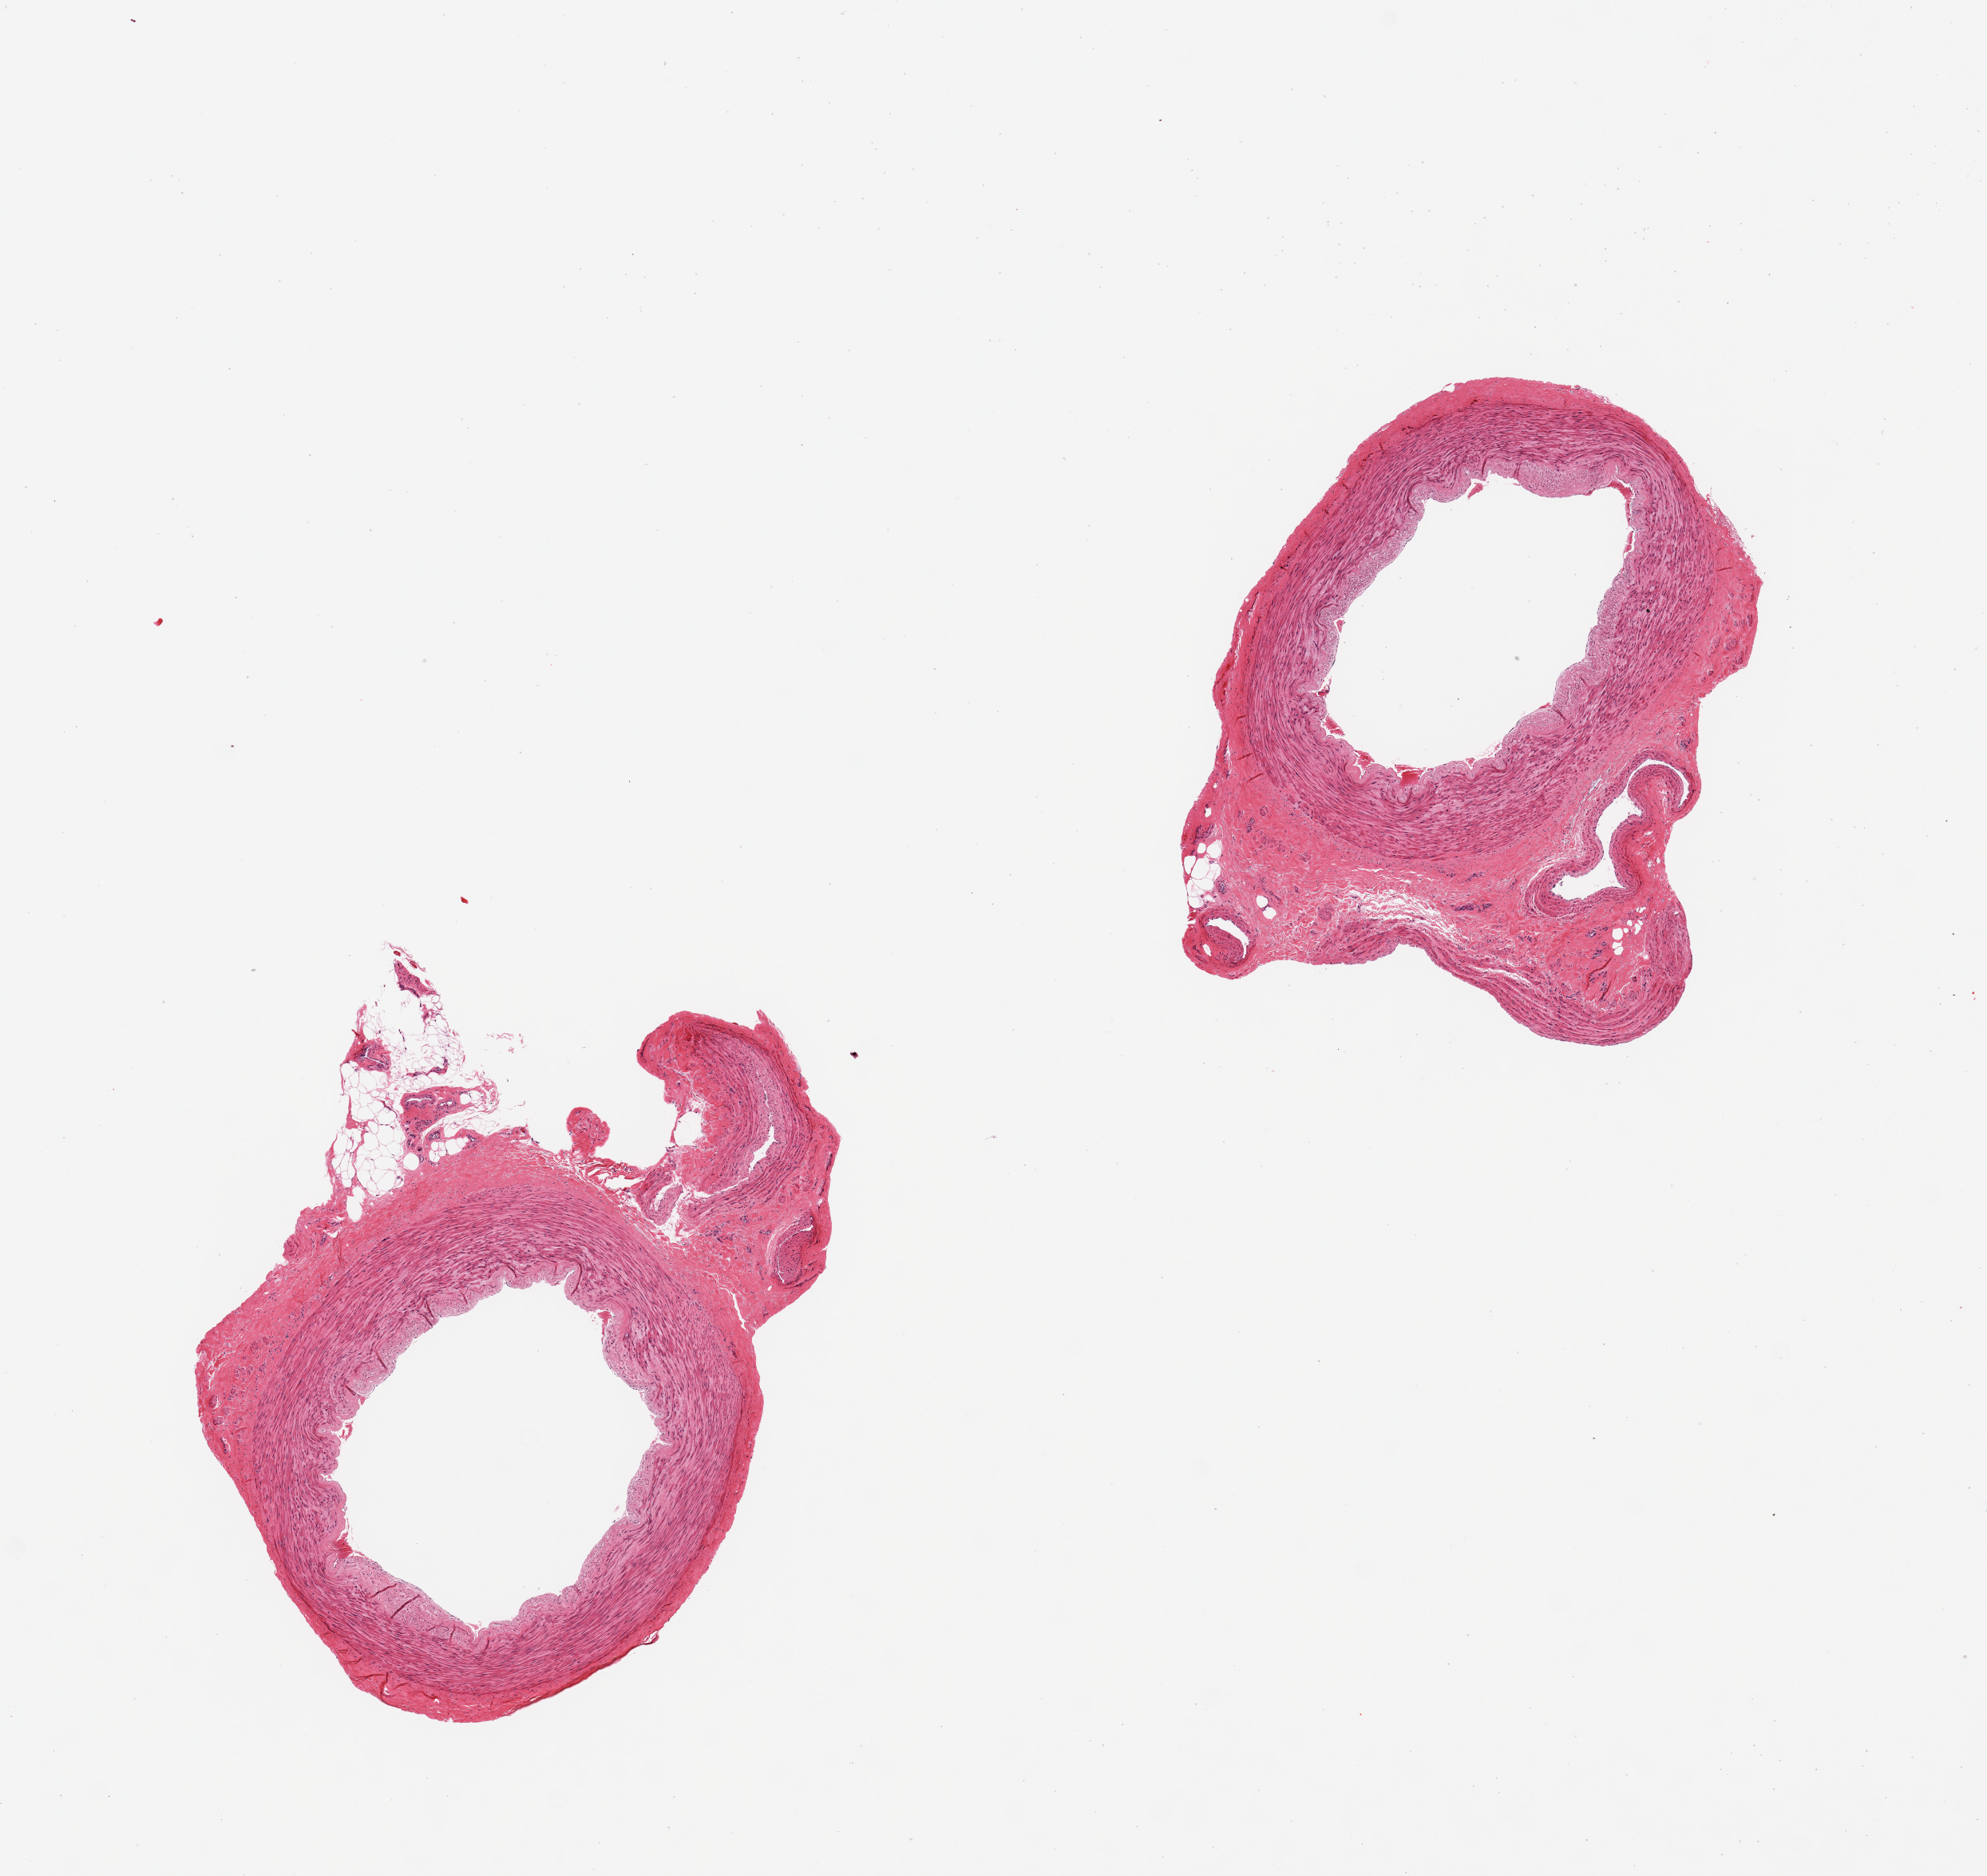
Digitized haematoxylin and eosin-stained section, brightfield — whole scanned area (about 9.8 x 9.3 mm, acquisition: 20x scan) shown as a low-resolution overview, PAXgene-fixed paraffin-embedded (PFPE) section, sampled site (target tissue): tibial artery, donor tissue sample. Donor: male.
Pathologist's review note for this sample: 2 pieces, some intimal thickening, 1.1mm attachment of fat.